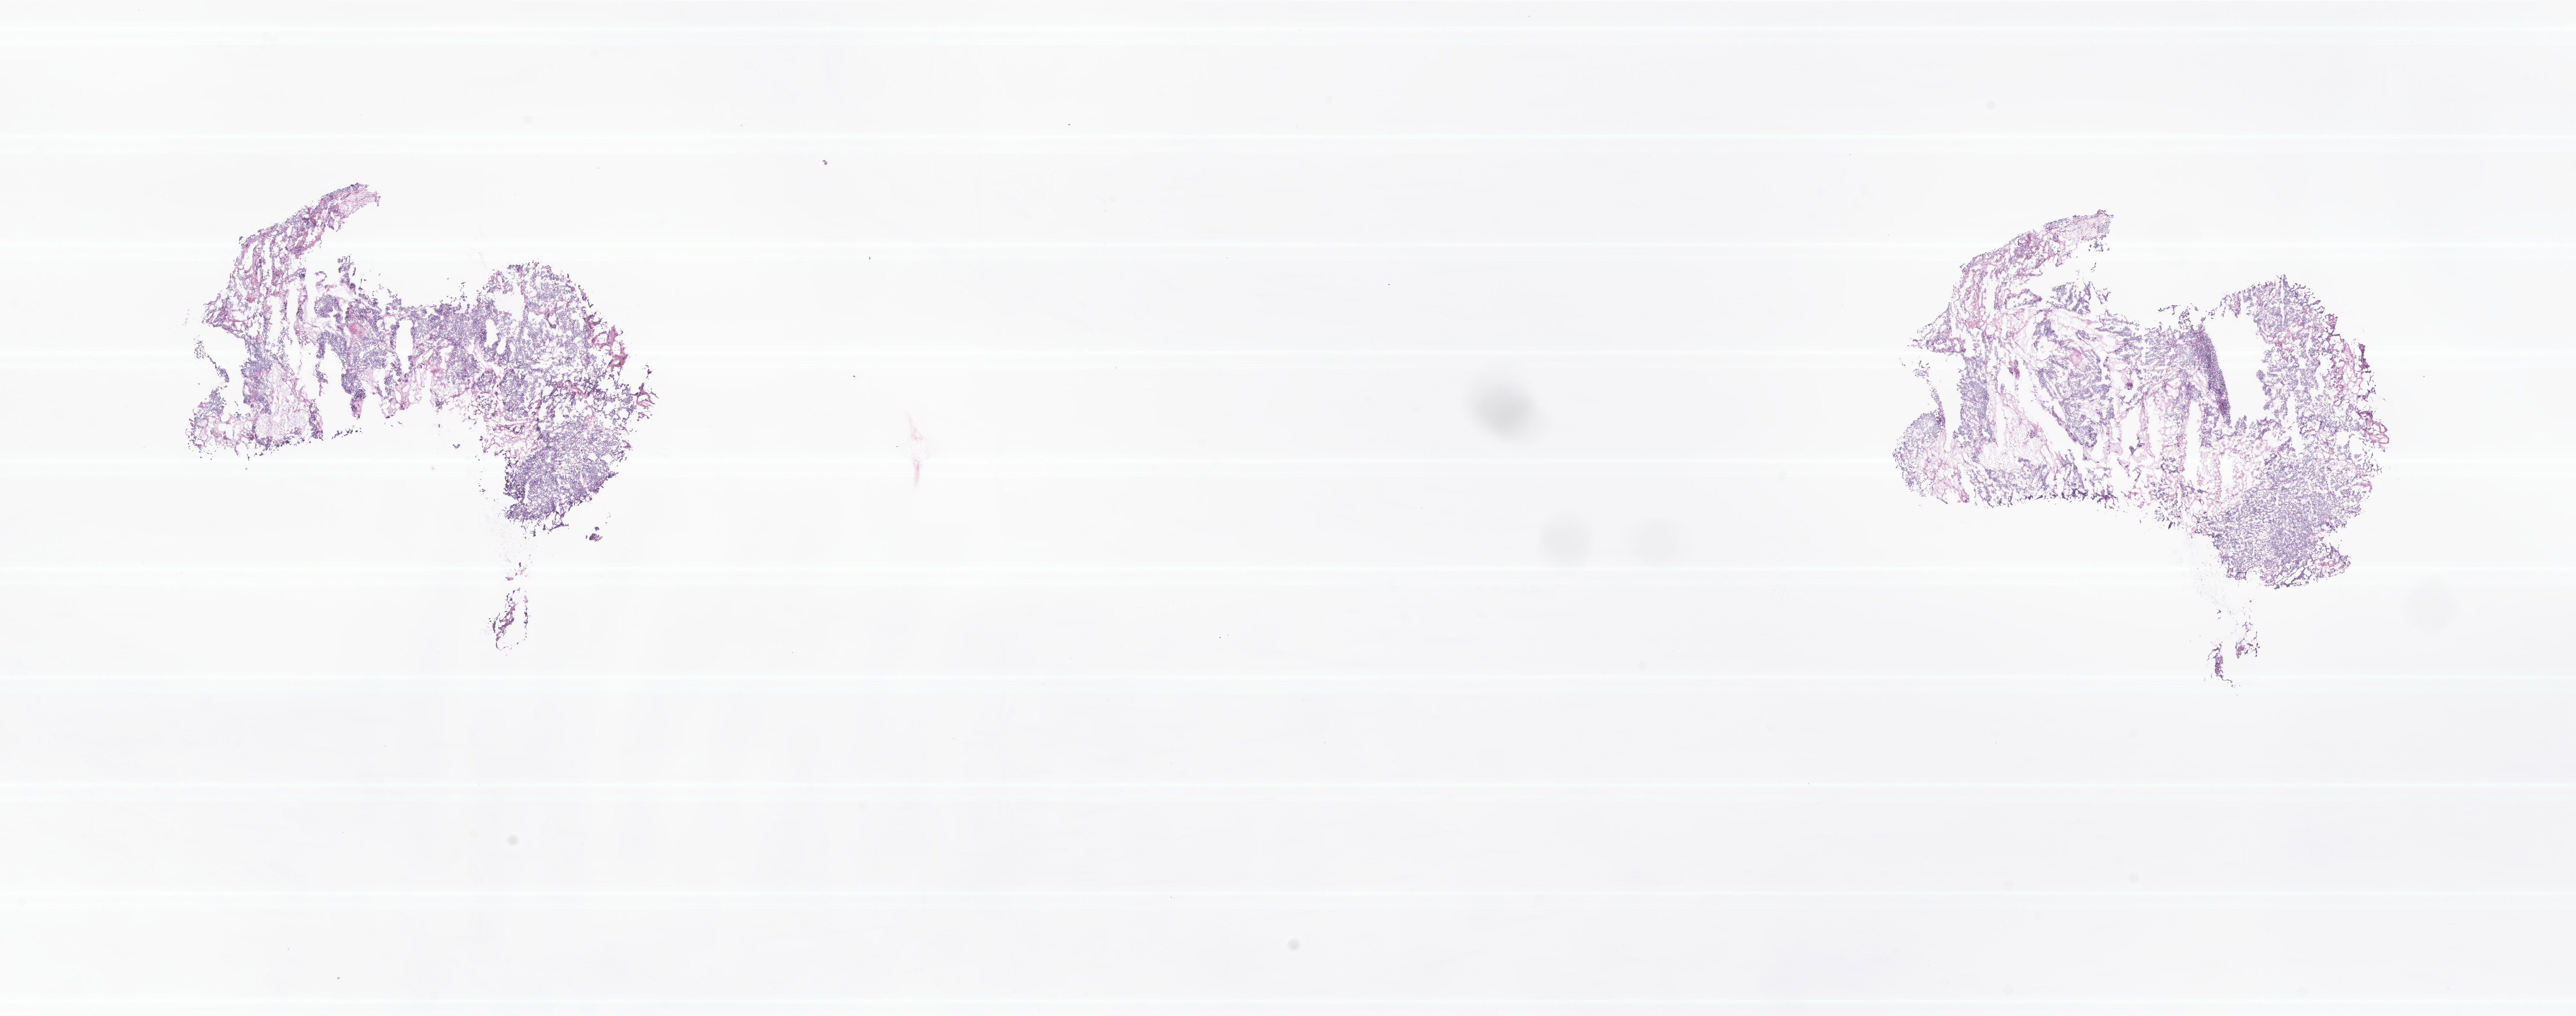
H&E whole-slide image of tumor tissue from the cerebral ventricle, whole scanned area (about 25.4 x 10.0 mm) shown as a low-resolution overview. Frozen section. Patient: male, age 74 months.
Diagnosis: Medulloblastoma, NOS.